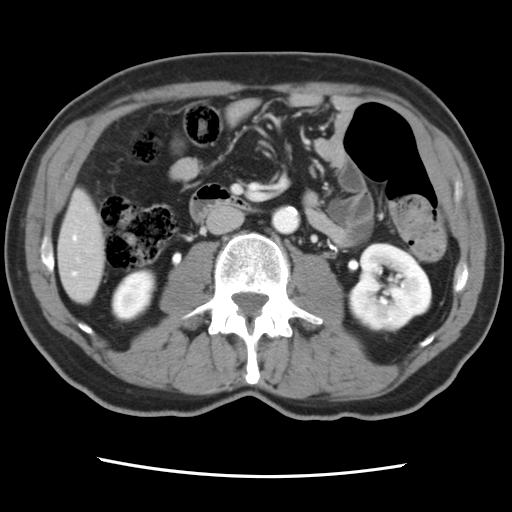
Contrast-enhanced abdominal CT, one axial slice; slice 21 of 83 in the series (ordered by position); soft-tissue window (W 400 / L 40 HU); 5 mm slice thickness; 512 × 512 image matrix, field of view 321 × 321 mm. Male patient, age 69 years. From the clinical record (not read from this slice): diagnosis: colorectal cancer liver metastases, imaged before liver resection; multiple liver metastases: yes; largest metastasis: 3.5 cm.
Outlined on this slice (expert manual segmentation):
- hepatic veins: box from (x=73, y=236) to (x=77, y=276) px
- liver: (x=59, y=193)–(x=106, y=303)
- planned liver remnant (the part of the liver to remain after resection): (x=59, y=193)–(x=106, y=302)